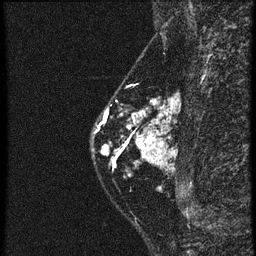
Breast MRI (dynamic contrast-enhanced), one sagittal slice; 4 images stored at this slice position (order not interpretable as contrast timing); 1.5 T; TE 4.2 ms, TR 20.4 ms; 1.5 mm slice thickness; 256 × 256 image matrix, field of view 180 × 180 mm. Patient: female, 46 years. Case-level facts recorded for this patient, not image findings: setting: breast cancer imaged before/during neoadjuvant chemotherapy; receptor status: triple-negative.
Annotated regions visible in this slice (semi-automatic segmentation, software-assisted and operator-edited):
- analysis volume of interest (the breast-tissue region the enhancement analysis was run in; not a lesion): box from (x=90, y=82) to (x=165, y=185) px
- tumour enhancement mask (voxels above the 90 % enhancement threshold inside the analysis volume of interest): (x=96, y=122)–(x=159, y=161)